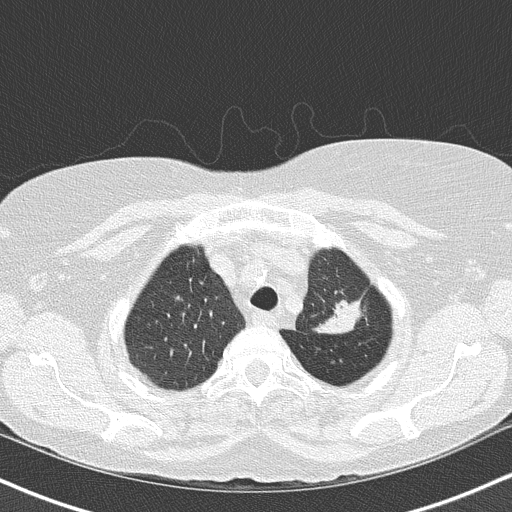
Low-dose screening chest CT, one axial slice; slice 126 of 147 in the series (ordered by position); 120 kVp; lung window (W 1500 / L -600 HU); 2 mm slice thickness; 512 × 512 image matrix, field of view 320 × 320 mm.
Annotated regions visible in this slice (outlined manually by an expert reader):
- lesion 1 (tumor, upper lobe of left lung): box from (x=316, y=301) to (x=361, y=334) px